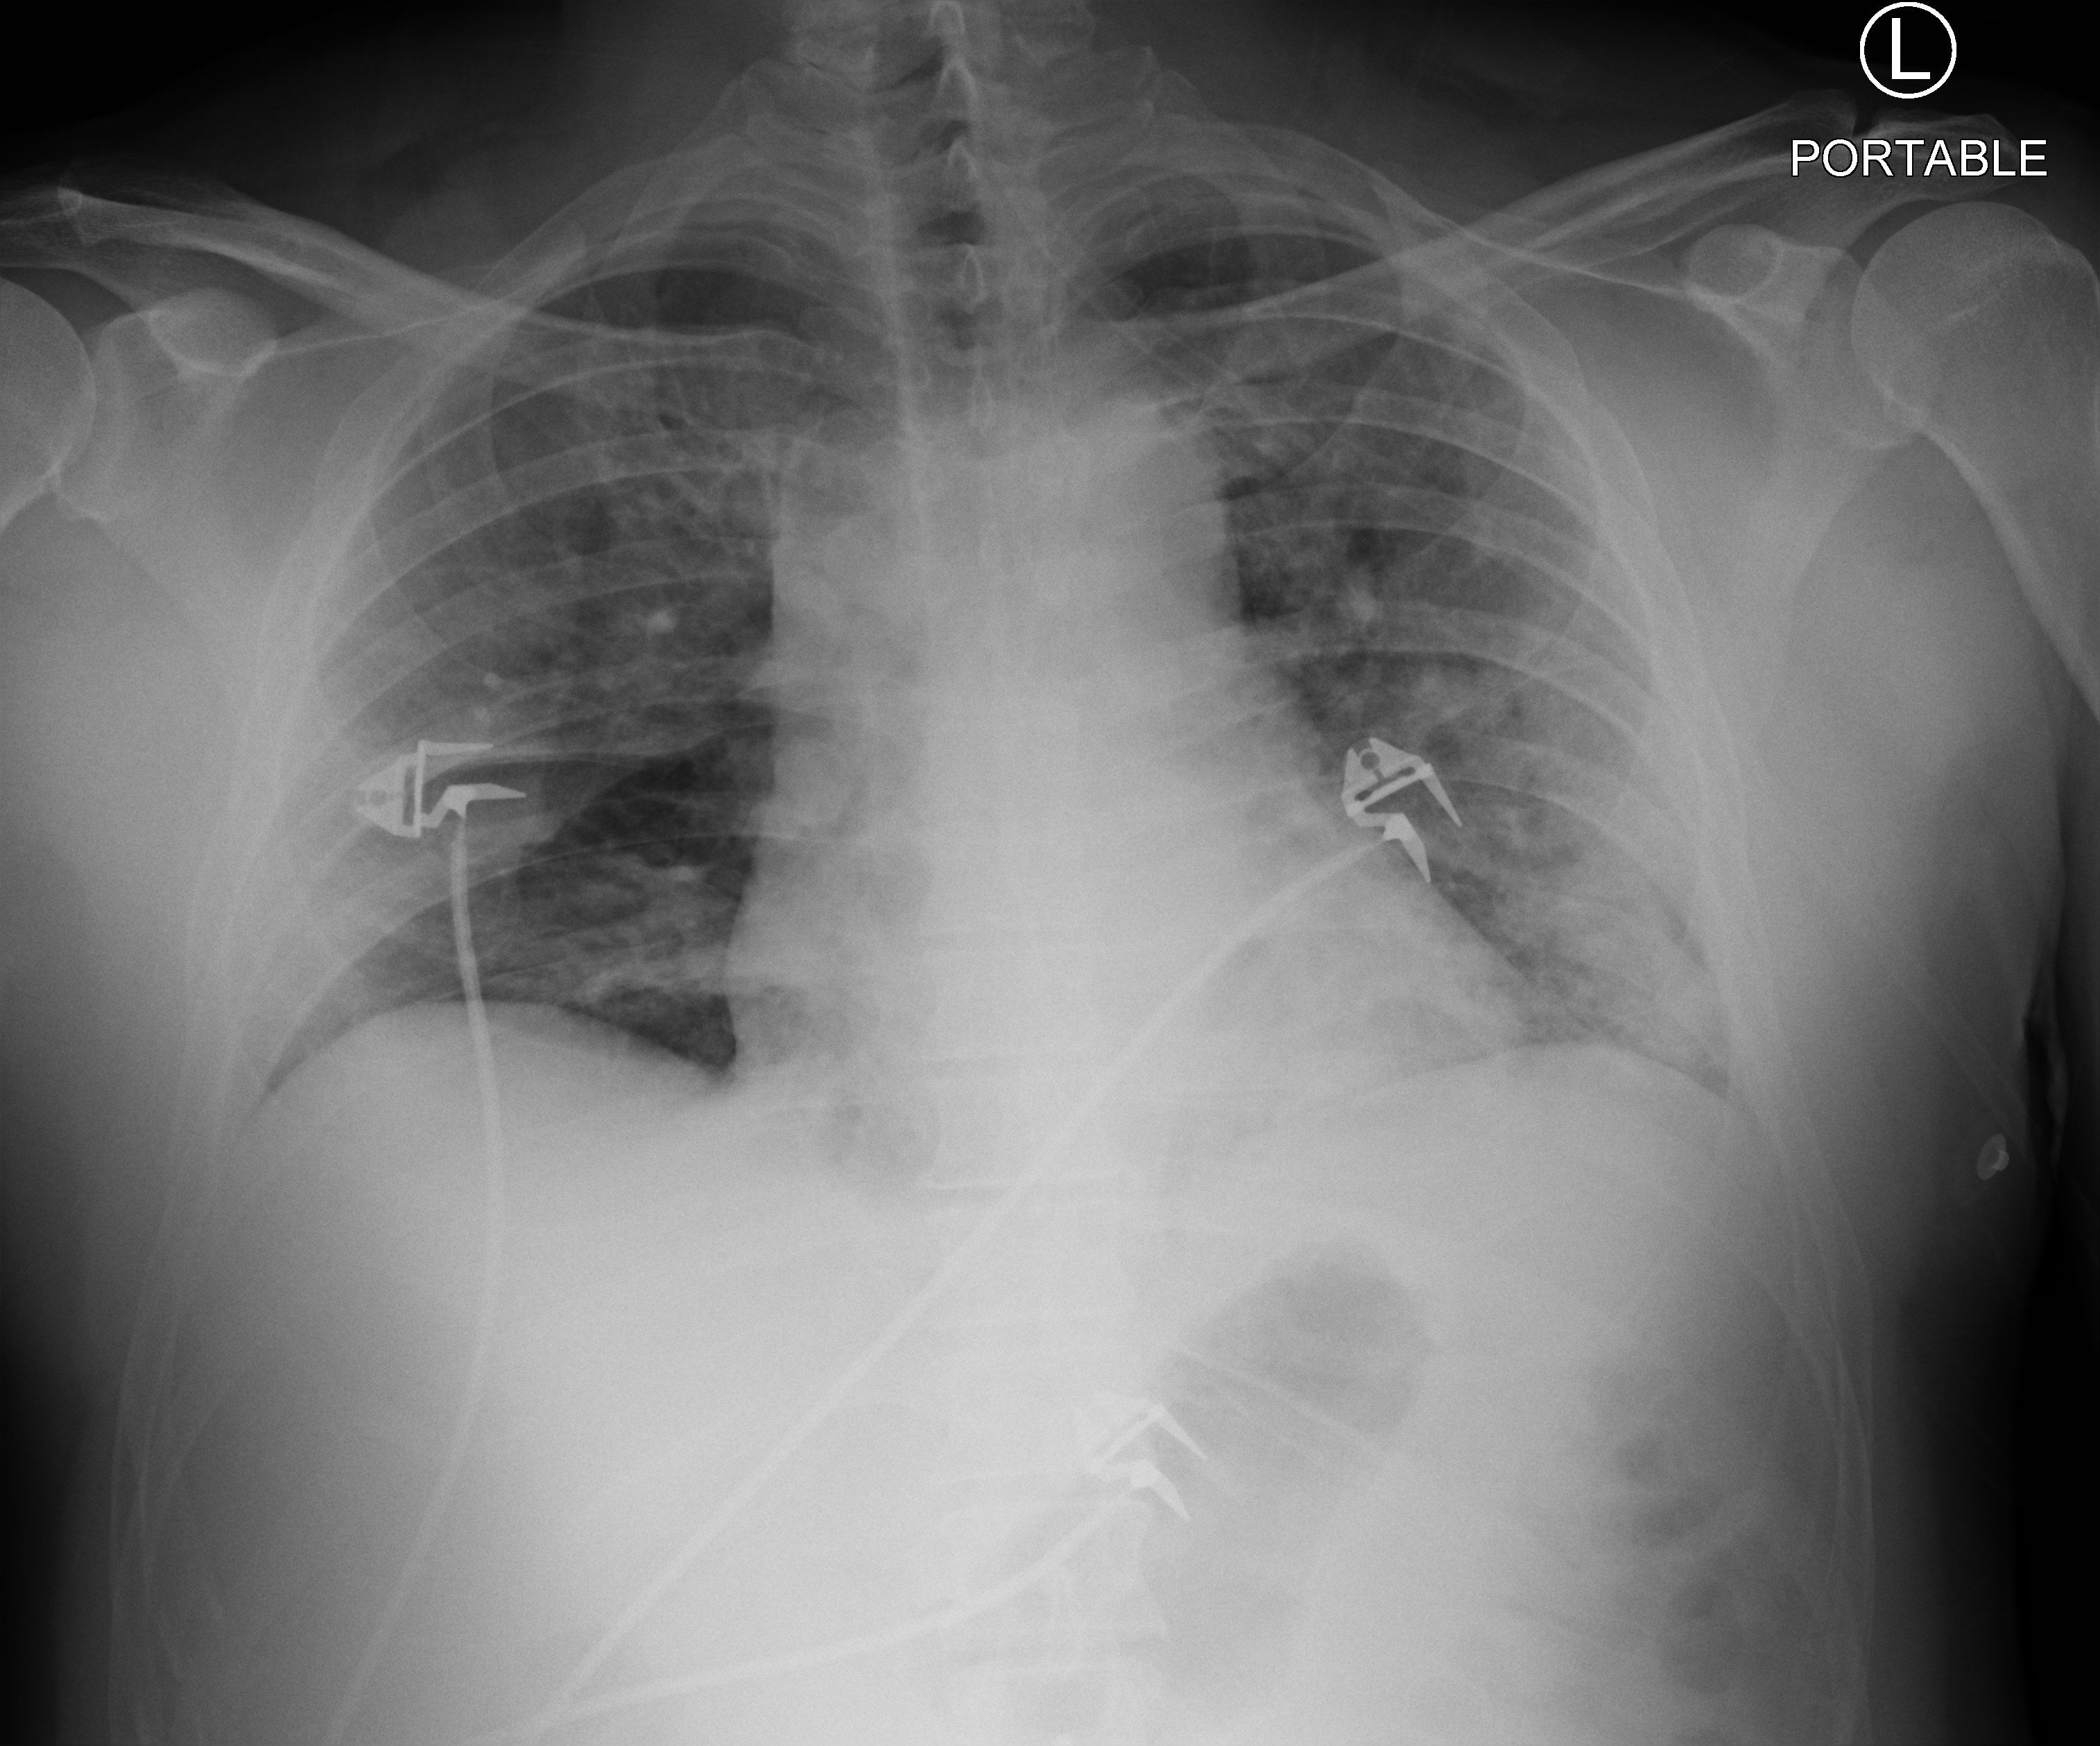
Chest X-ray (portable), anteroposterior (AP) projection. Male patient hospitalised with COVID-19, age 18–59 years.
From the hospital-stay record, not from the radiograph (when in the stay this image was taken is not recorded): admitted to intensive care during this hospital stay: yes; length of hospital stay: 24 days; mechanically ventilated during this hospital stay: no.